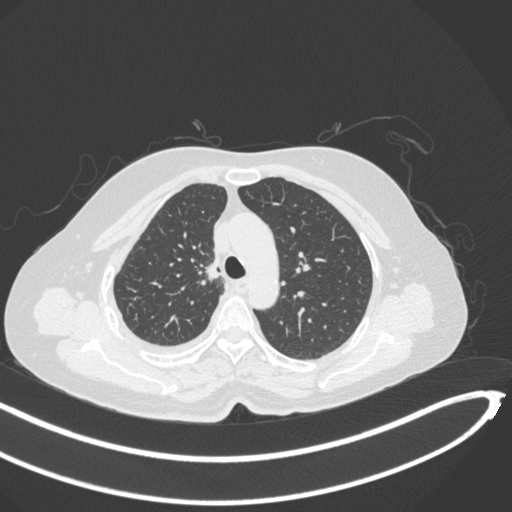
Chest CT, one axial slice; position 224 of 297 along the scan axis; 120 kVp; lung window (W 1500 / L -600 HU); 1 mm slice thickness; 512 × 512 image matrix. Female patient, age 64 years. From the clinical record (not read from this slice): clinical TNM (as recorded): T1b N0 M1.
Structures marked on this image (bounding box drawn by a radiologist):
- lung tumour (recorded histology: adenocarcinoma): bounding box <202,258,224,285> (left, top, right, bottom; pixels)